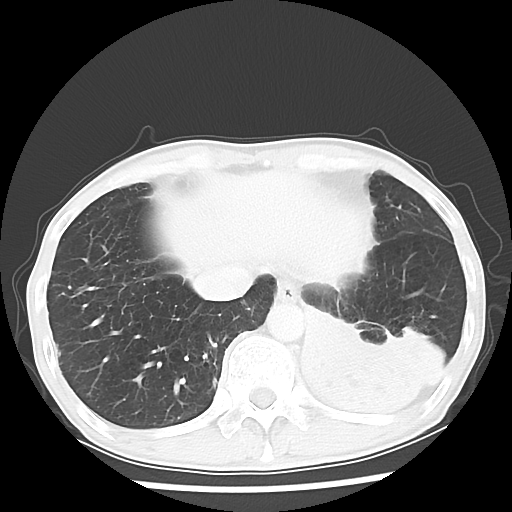
Chest CT, one axial slice. Slice 12 of 64 in the series (ordered by position). 120 kVp. Lung window (W 1500 / L -600 HU). 512 × 512 image matrix. Patient: male, 68 years. From the clinical record (not read from this slice): clinical TNM (as recorded): T4 N0 M0.
Outlined on this slice (rectangle marked by the reading radiologist):
- lung tumour (recorded histology: squamous cell carcinoma): bounding box <299,327,437,424> (left, top, right, bottom; pixels)